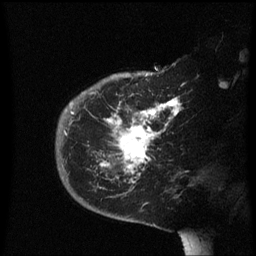
Breast MRI (dynamic contrast-enhanced), one sagittal slice. Slice 42 of 60 in the series (ordered by position). Dynamic contrast-enhanced series, image 2 of 3 at this slice position (ordered by acquisition). 1.5 T. TE 4.2 ms, TR 8.4 ms. 2.3 mm slice thickness. 256 × 256 image matrix, field of view 200 × 200 mm. Female patient, age 38 years. Case-level facts recorded for this patient, not image findings: setting: breast cancer imaged before/during neoadjuvant chemotherapy; receptor status: HER2-positive.
Structures marked on this image (semi-automatically segmented with operator editing):
- analysis volume of interest (the breast-tissue region the enhancement analysis was run in; not a lesion): bounding box <56,78,191,213> (left, top, right, bottom; pixels)
- tumour enhancement mask (voxels above the 70 % enhancement threshold inside the analysis volume of interest): <70,98,180,189>